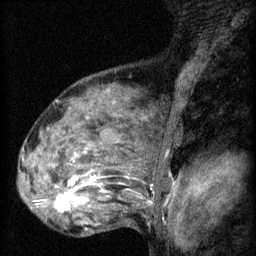
Breast MRI (dynamic contrast-enhanced), one sagittal slice. Slice 42 of 60 in the series (ordered by position). 3 images stored at this slice position (order not interpretable as contrast timing). 1.5 T. TE 4.2 ms, TR 8.2 ms. 2 mm slice thickness. 256 × 256 image matrix. Female patient, age 48 years.
Outlined on this slice (semi-automatically segmented with operator editing):
- analysis volume of interest (the breast-tissue region the enhancement analysis was run in; not a lesion): bounding box (x1, y1, x2, y2) in pixels: (48, 160, 125, 217)
- tumour enhancement mask (voxels above the 70 % enhancement threshold inside the analysis volume of interest): (54, 178, 77, 213)